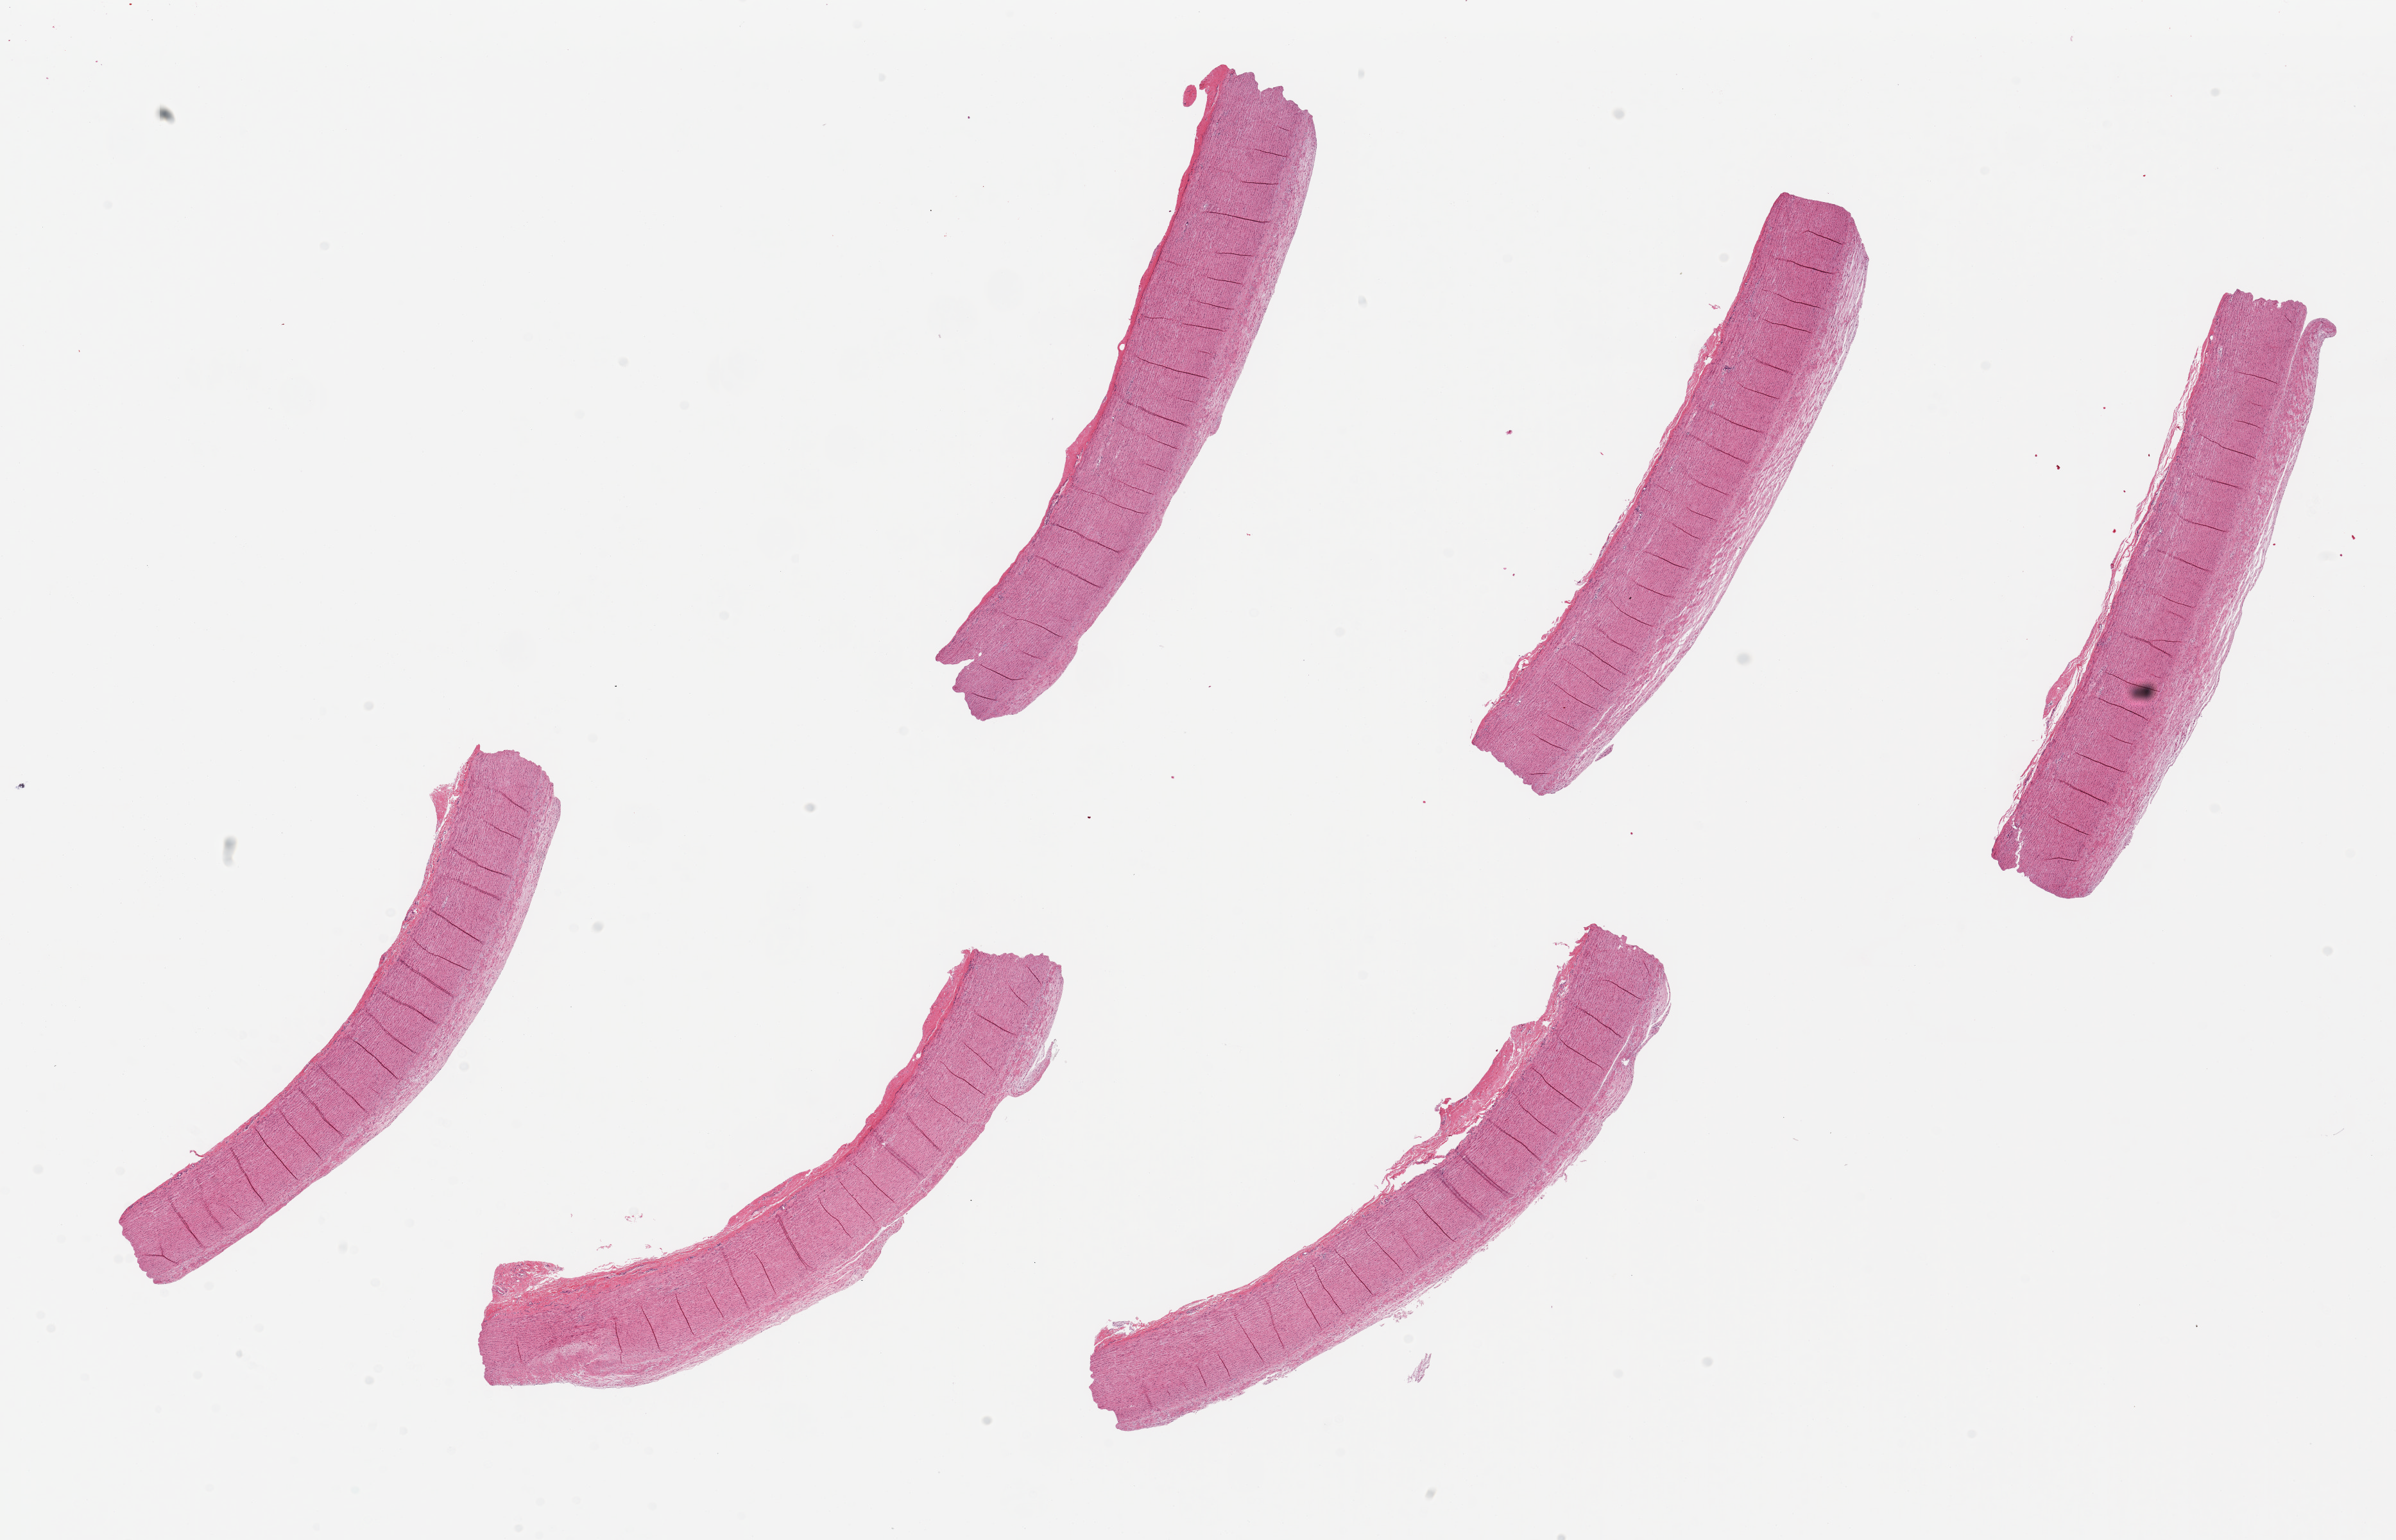
Whole-slide image, hematoxylin and eosin (H&E) stain, whole scanned area (about 29.5 x 19.0 mm) shown as a low-resolution overview; PAXgene-fixed, paraffin-embedded tissue; sampled site (target tissue): aorta; donor tissue sample.
Pathologist's review note for this sample: 6 pieces ~8x1.5mm.